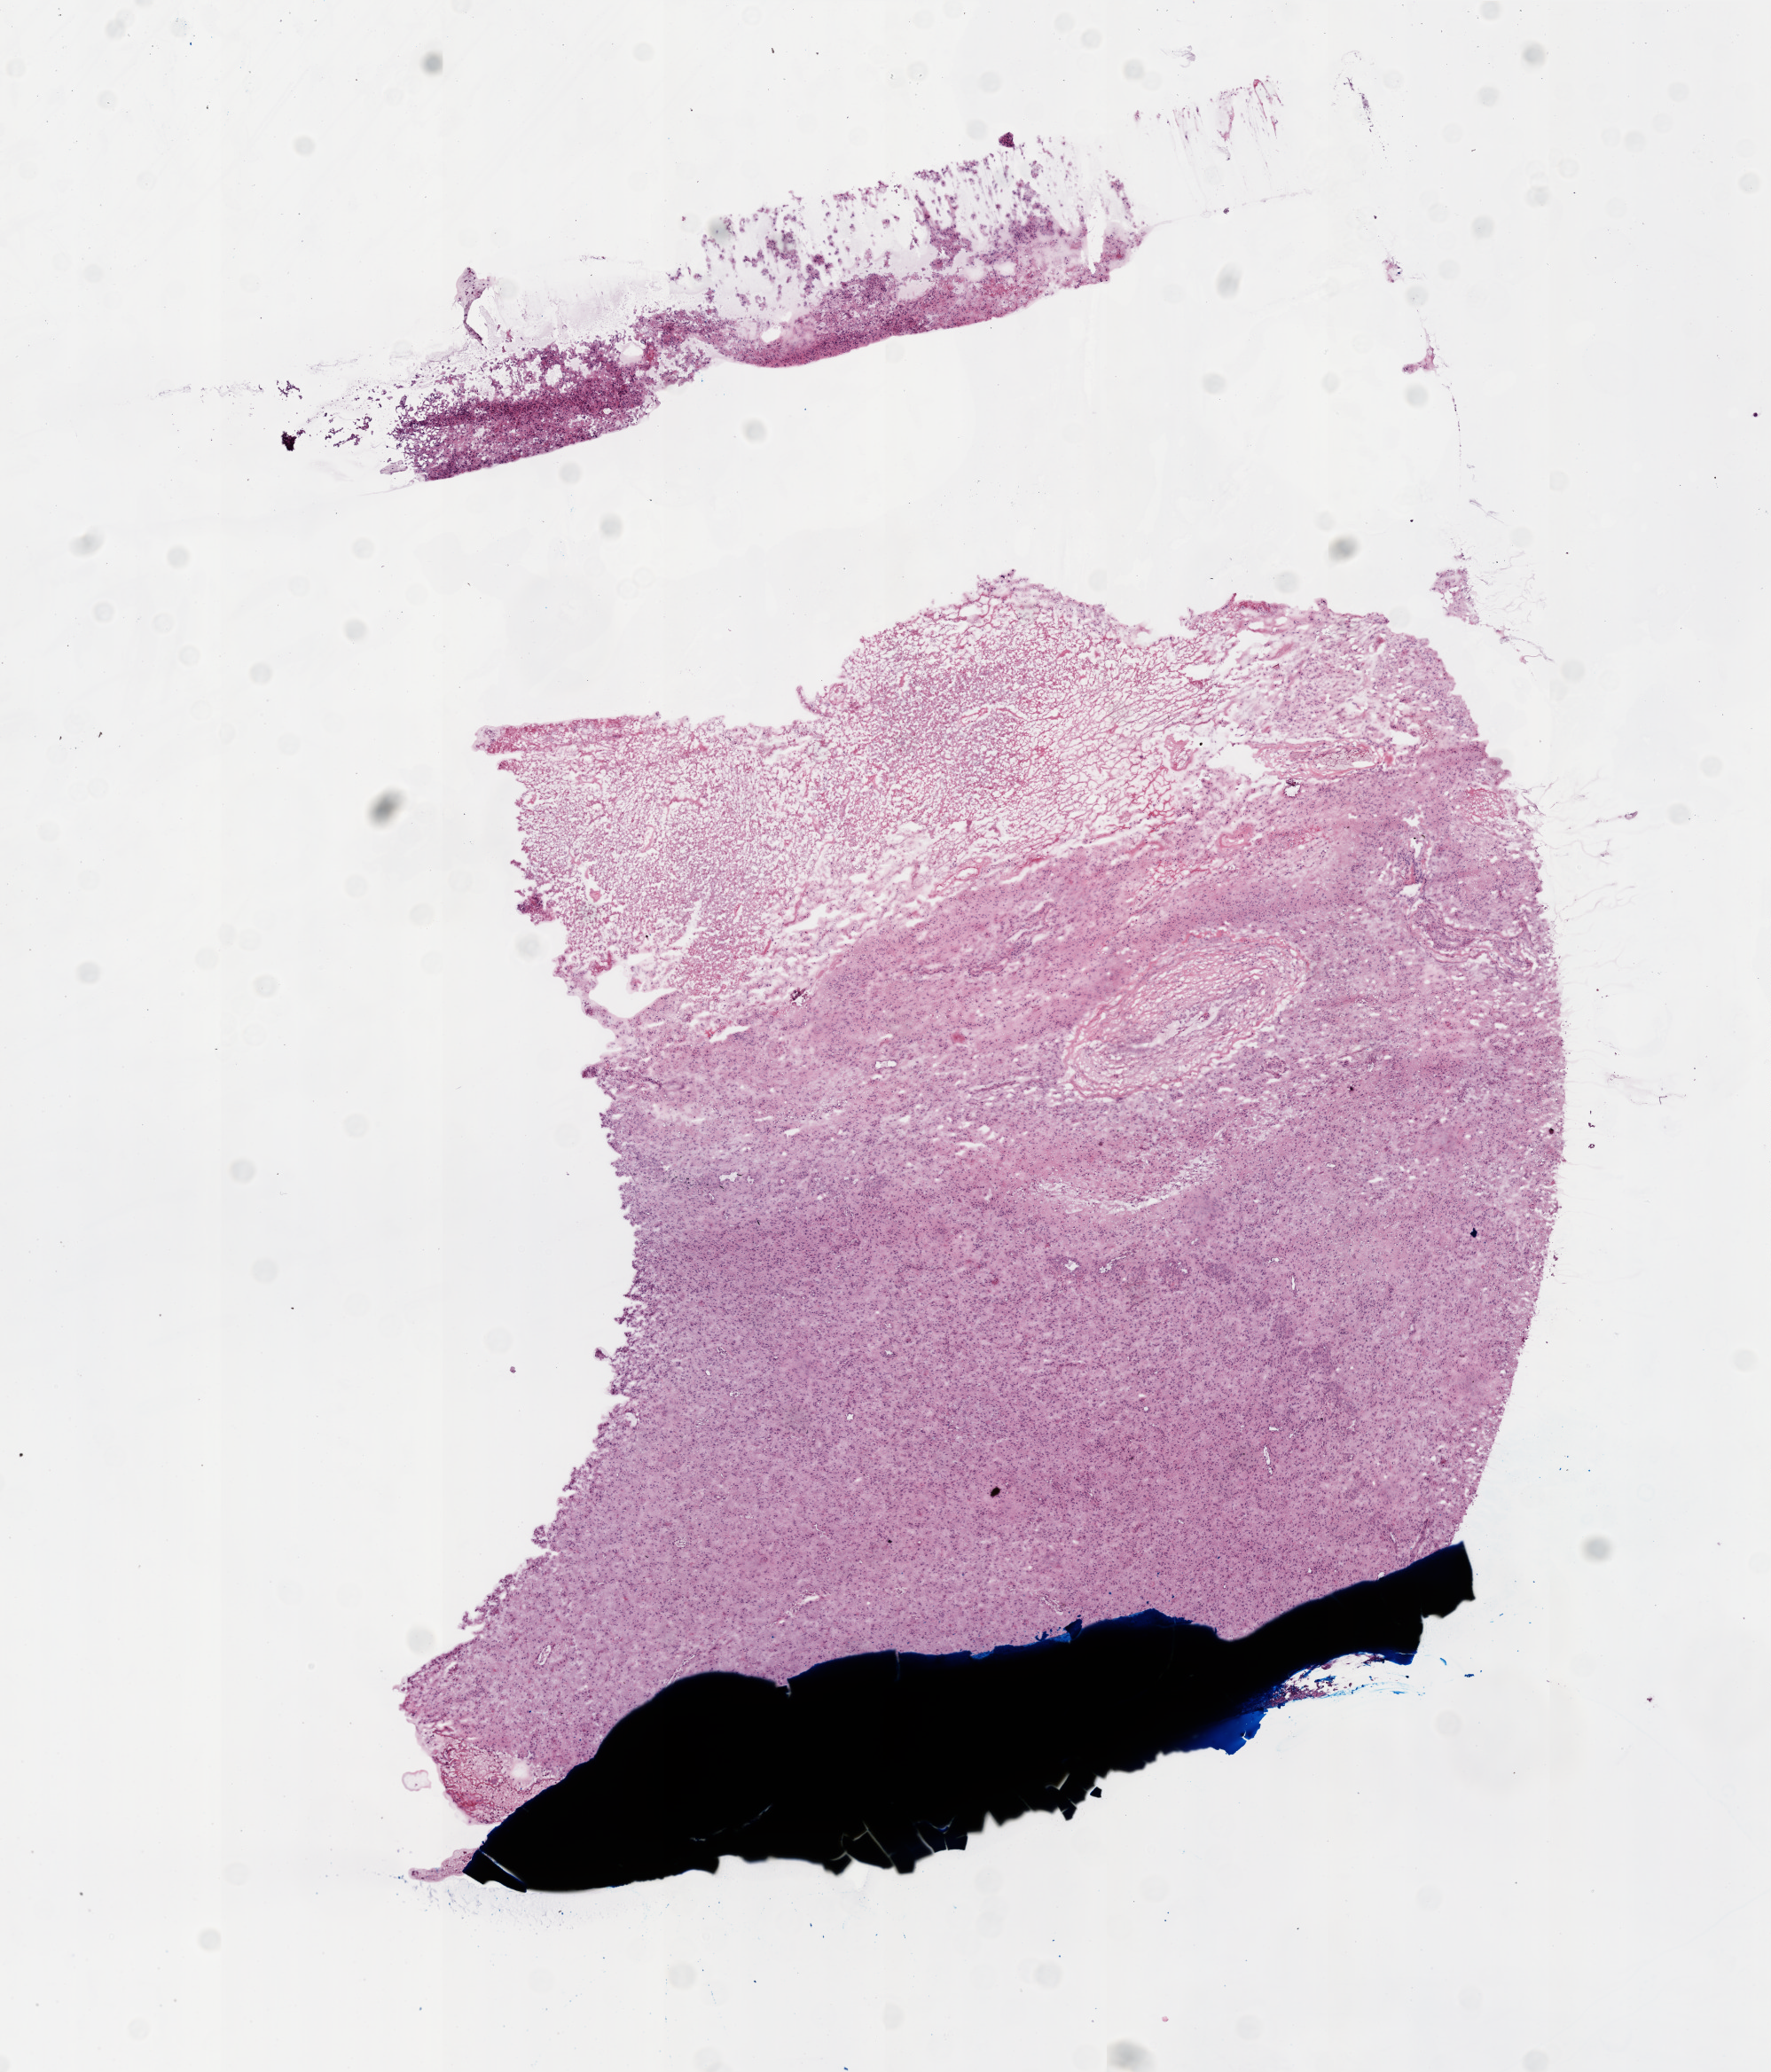
Whole-slide histology image, Hematoxylin and eosin (H&E) stained — a low-resolution overview of the entire scanned area, about 8.0 x 9.4 mm (from a 20x scan), frozen section from the top of the tissue portion, sample: primary tumour, brain. Male patient; age at initial diagnosis 50 years. Composition of this section per pathologist review: tumour cells 75%, tumour nuclei 100%, normal cells 0%, stromal cells 0%, necrosis 25%. Infiltration values recorded for this section: lymphocyte infiltration 0%.
Diagnosis: Glioblastoma.